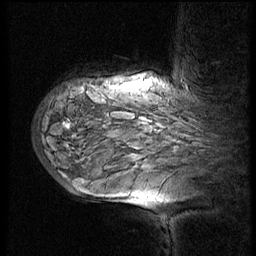
Breast MRI (dynamic contrast-enhanced), one sagittal slice; position 46 of 60 along the scan axis; 3 images stored at this slice position (order not interpretable as contrast timing); 1.5 T; TE 4.2 ms, TR 8.9 ms; 2.5 mm slice thickness; 256 × 256 image matrix. Patient: female, 57 years. From the clinical record (not read from this slice): setting: breast cancer imaged before/during neoadjuvant chemotherapy; receptor status: HER2-positive.
Outlined on this slice (semi-automatically segmented with operator editing):
- analysis volume of interest (the breast-tissue region the enhancement analysis was run in; not a lesion): box from (x=34, y=75) to (x=214, y=171) px
- tumour enhancement mask (voxels above the 140 % enhancement threshold inside the analysis volume of interest): (x=68, y=125)–(x=70, y=127)